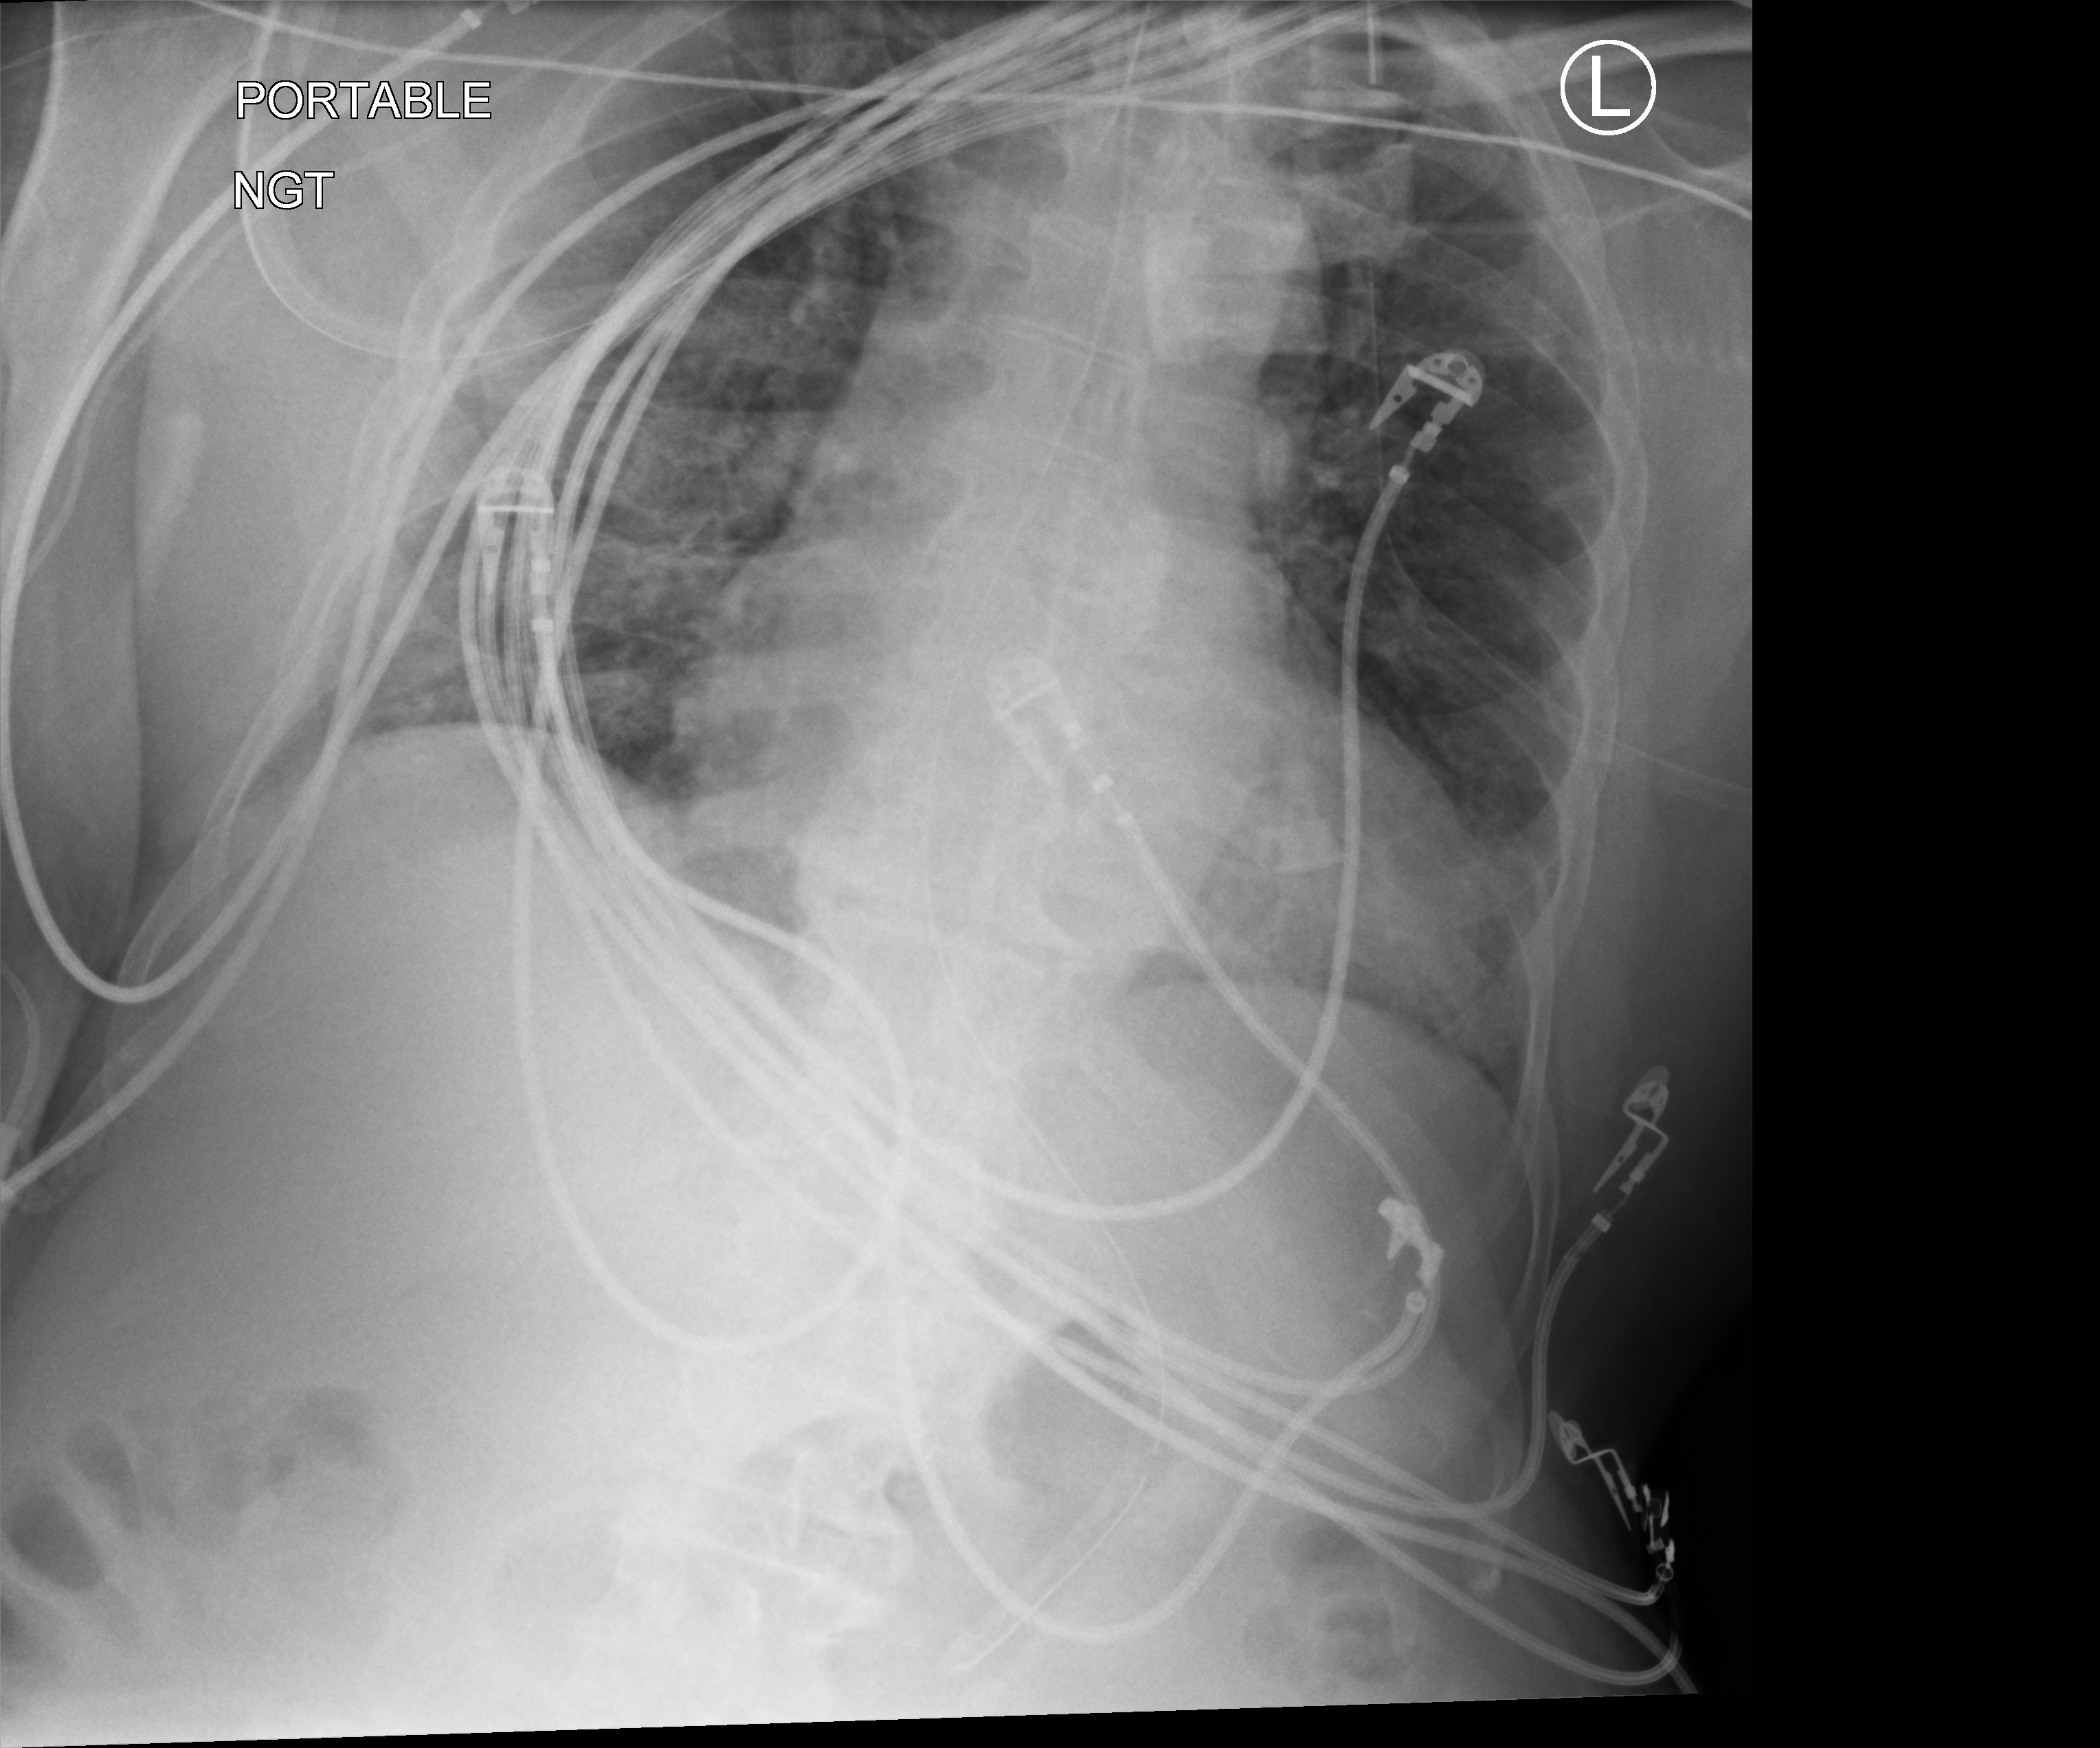
Portable chest radiograph, anteroposterior (AP) projection. Patient hospitalised with COVID-19; male, aged 60–74 years.
From the hospital-stay record, not from the radiograph (when in the stay this image was taken is not recorded): mechanically ventilated during this hospital stay: yes.